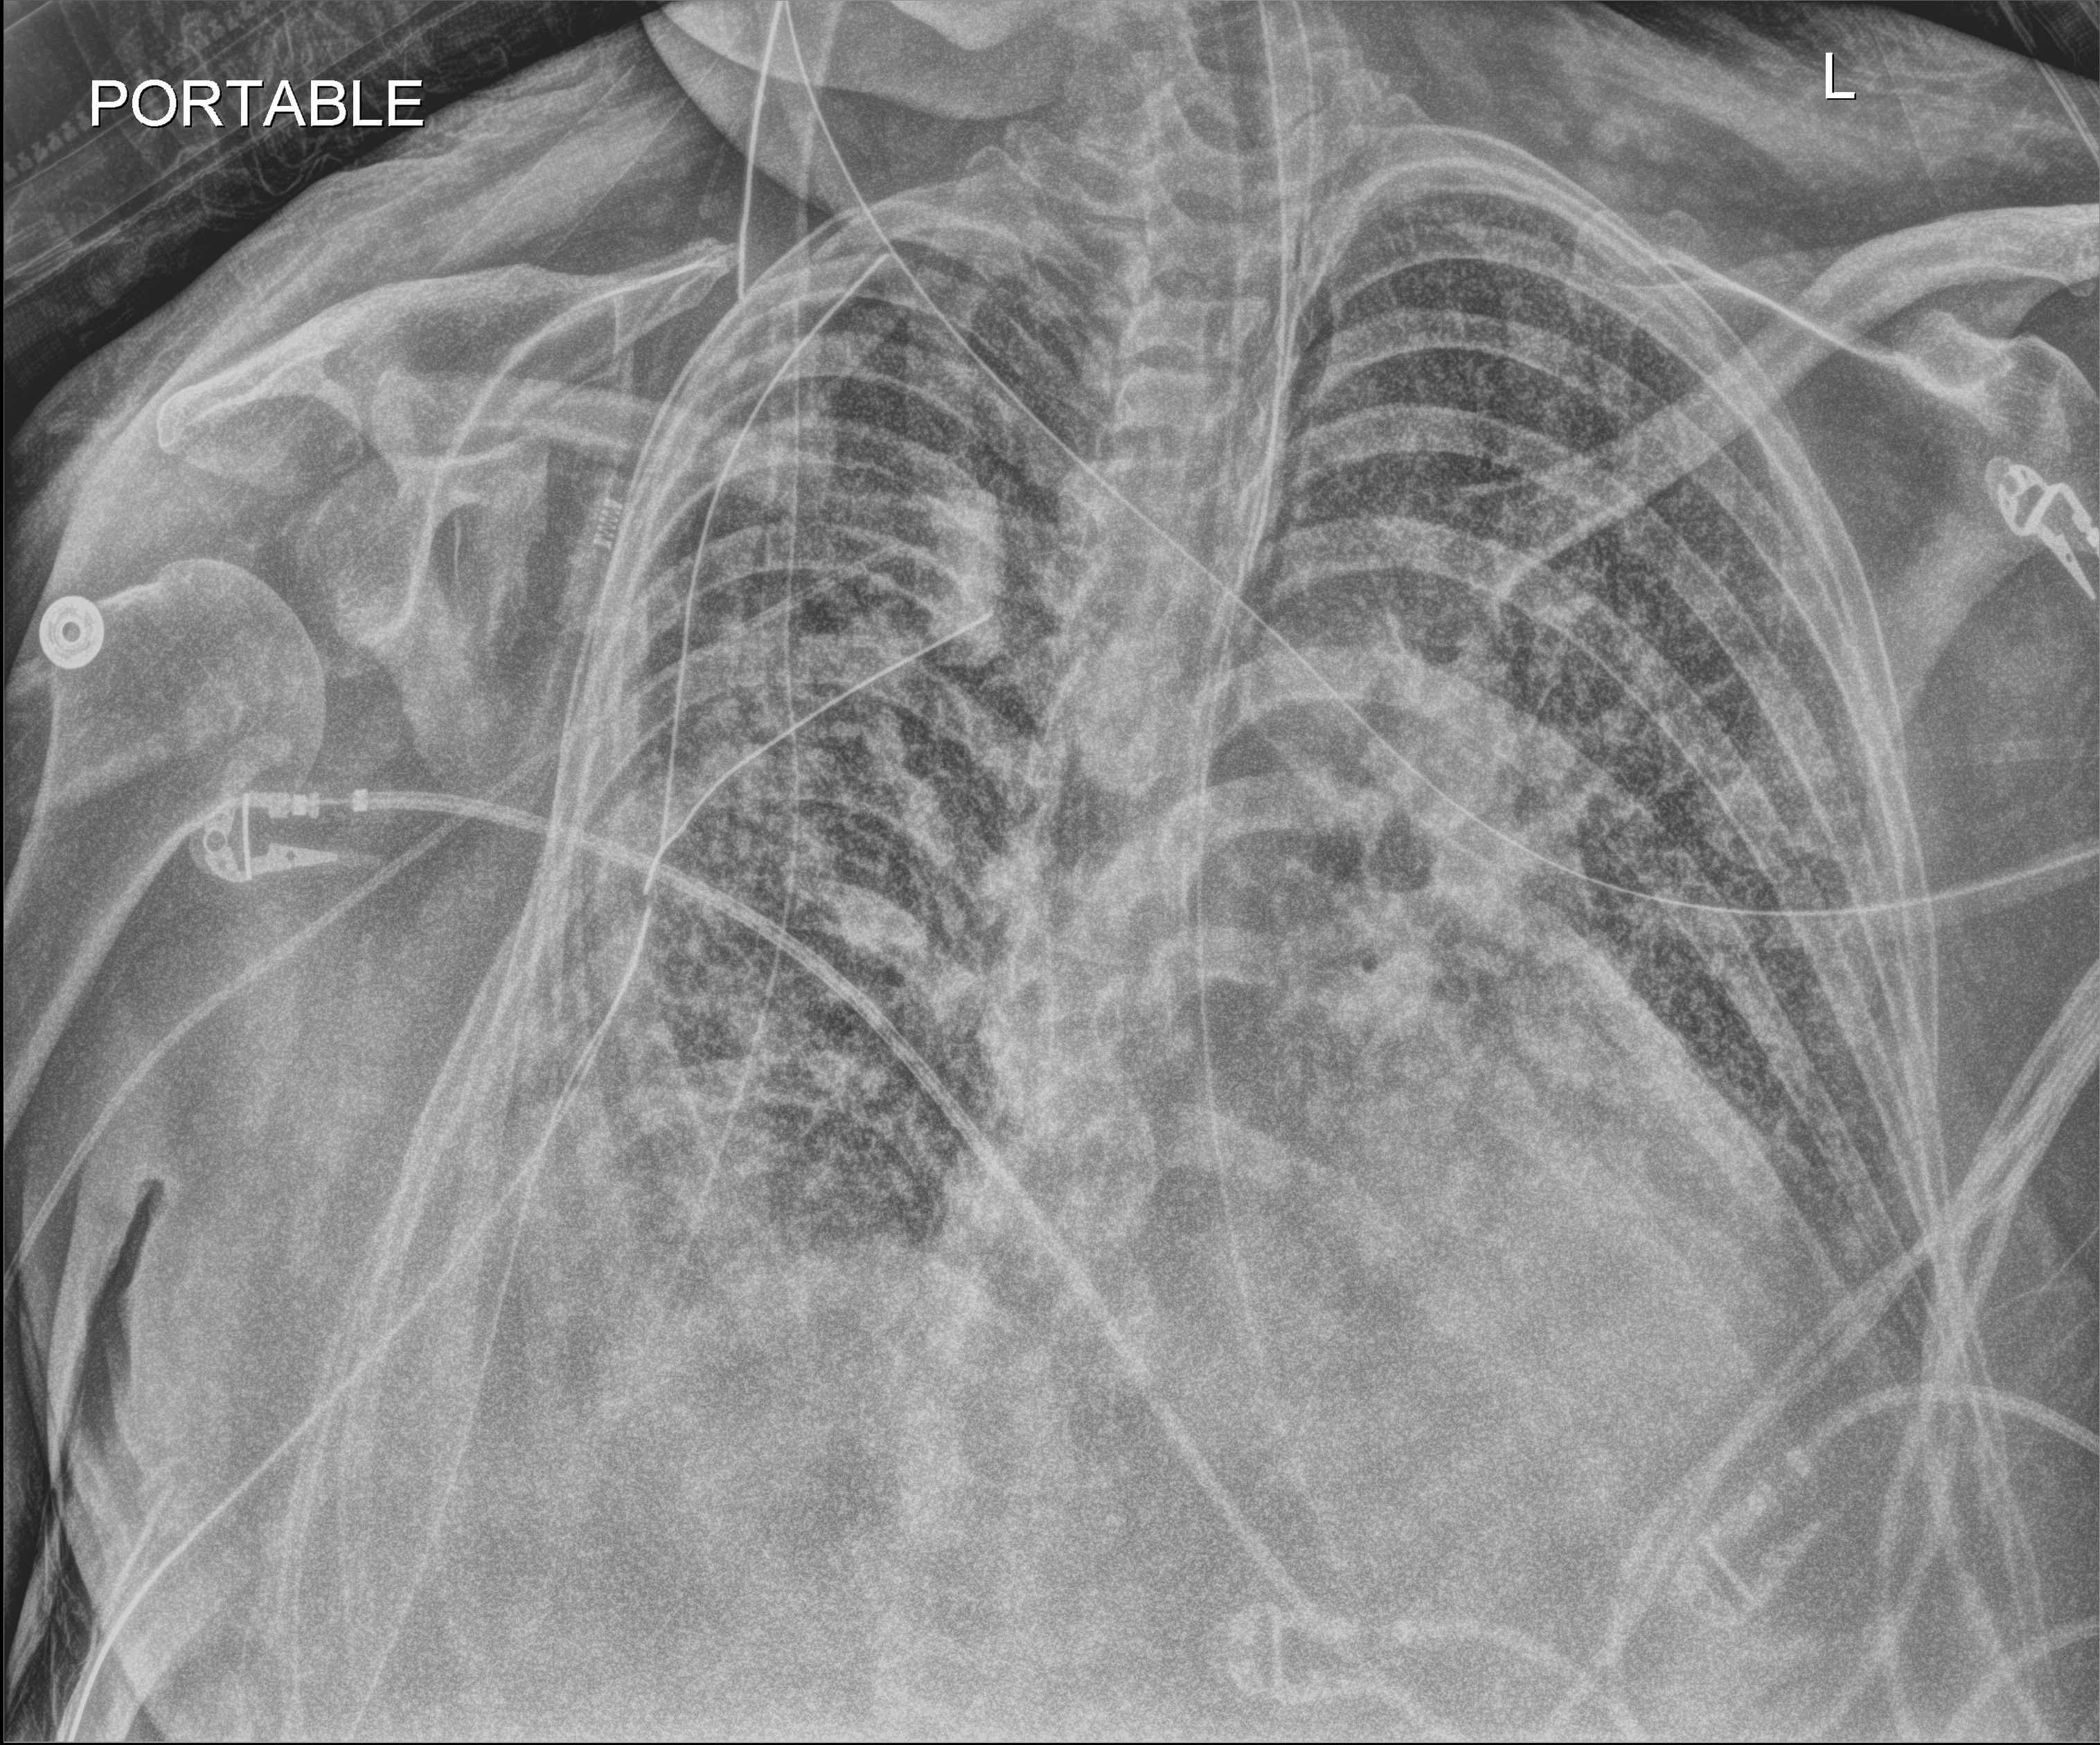
Portable chest radiograph, anteroposterior (AP) projection. Patient hospitalised with COVID-19, aged 18–59 years.
From the hospital-stay record, not from the radiograph (when in the stay this image was taken is not recorded):
- admitted to intensive care during this hospital stay: yes
- hypertension (admission record): no